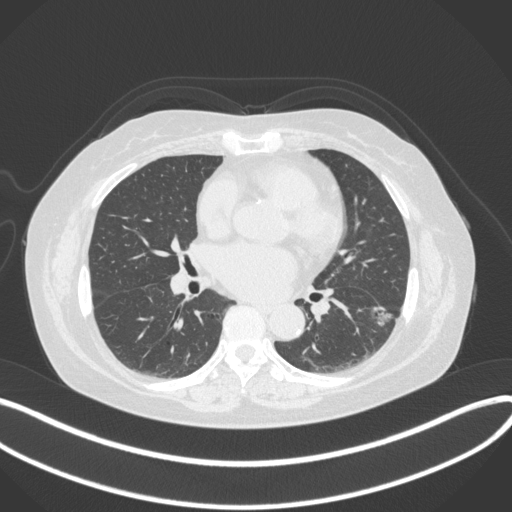
Chest CT, one axial slice. Position 175 of 373 along the scan axis. Lung window (W 1500 / L -600 HU). 512 × 512 image matrix, field of view 400 × 400 mm. Female patient, age 67 years. From the clinical record (not read from this slice): clinical TNM (as recorded): T1c N0 M0.
Structures marked on this image (rectangle marked by the reading radiologist):
- lung tumour (recorded histology: adenocarcinoma): bounding box (x1, y1, x2, y2) in pixels: (365, 297, 399, 333)